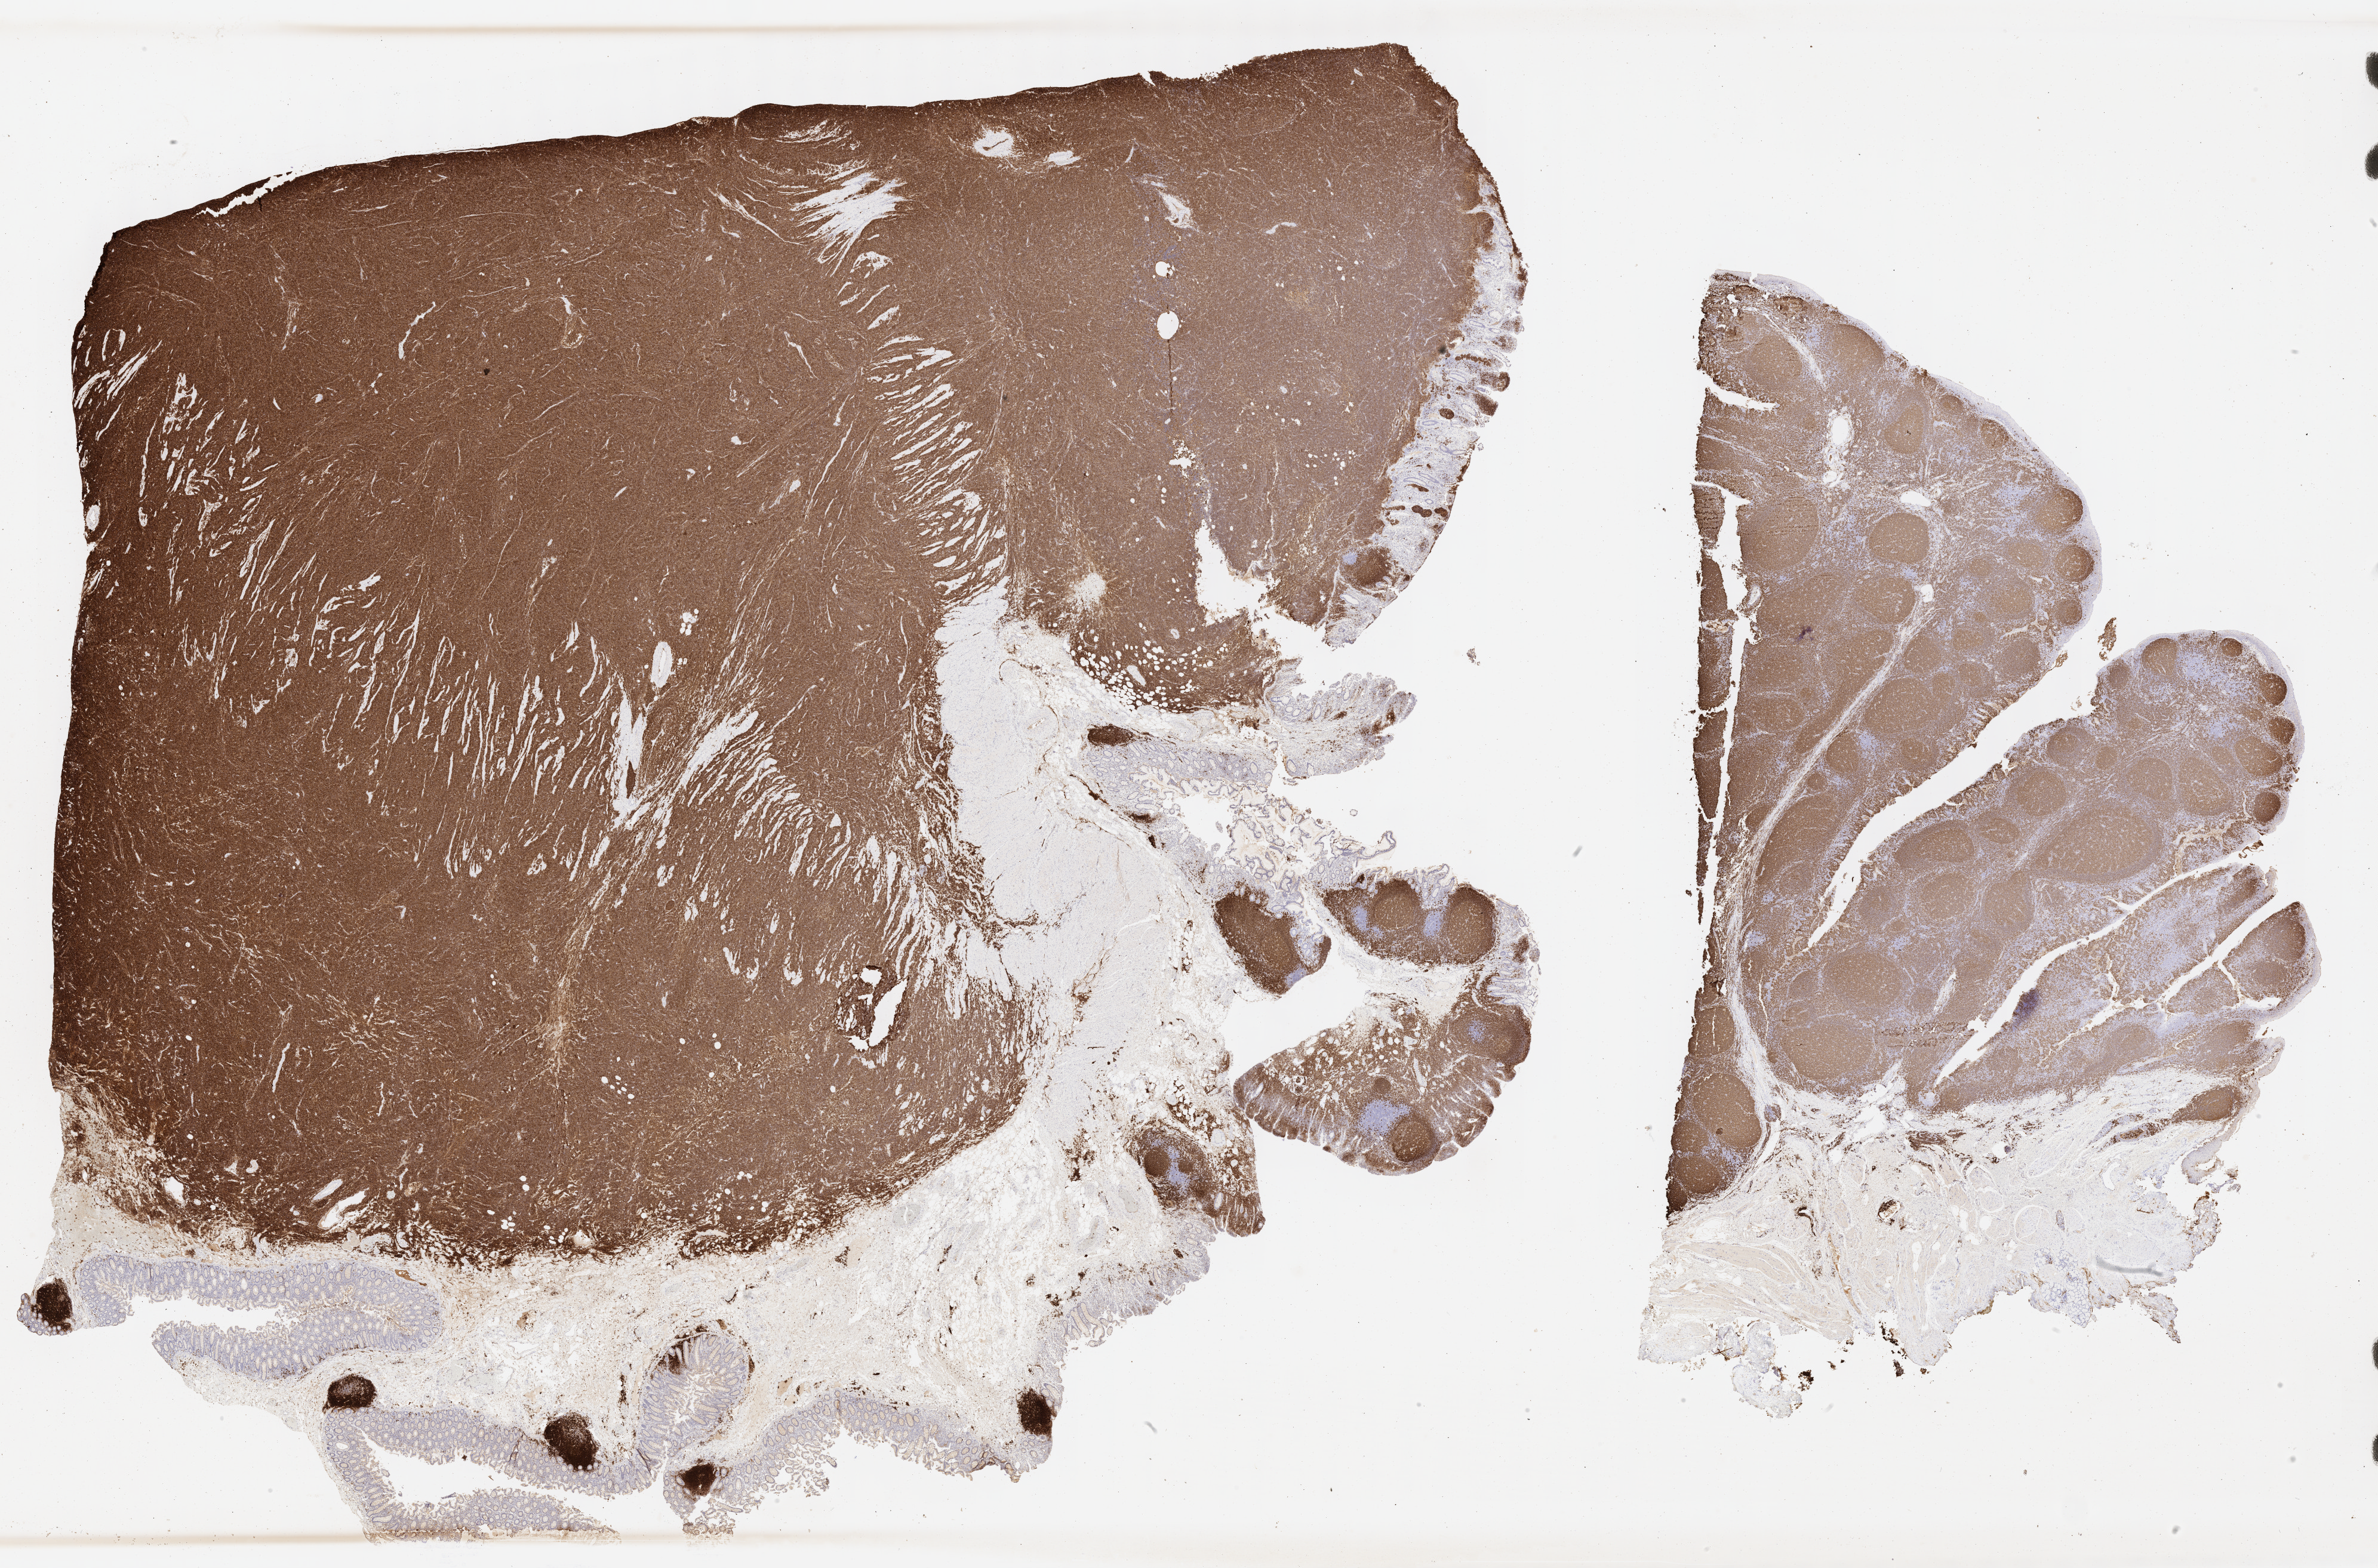
Immunohistochemistry (IHC) whole-slide image stained for CD20 — a low-resolution overview of the entire scanned area, about 32.2 x 21.2 mm; specimen: tumor tissue. Patient: male, aged 59.
Diagnosis: Burkitt lymphoma, NOS.